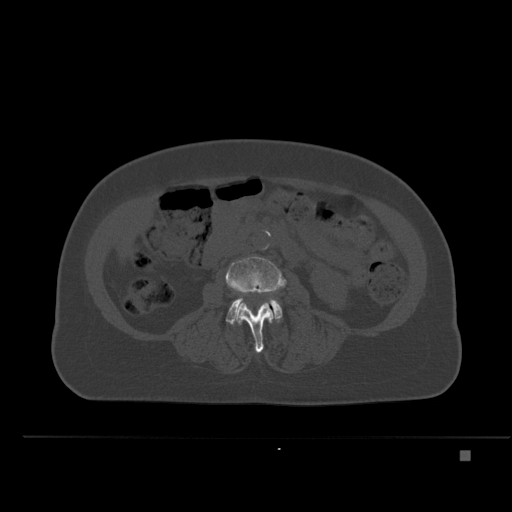
CT including the spine, one axial slice. Slice 191 of 477 in the series (ordered by position). Bone window (W 1800 / L 400 HU). 1.5 mm slice thickness. 512 × 512 image matrix, field of view 422 × 422 mm. Female patient, age 74 years. From the clinical record (not read from this slice): primary cancer: colon.
Annotated regions visible in this slice (semi-automatic segmentation, software-assisted and operator-edited):
- L3 vertebra: bounding box (x1, y1, x2, y2) in pixels: (225, 257, 287, 353)
- L4 vertebra: (226, 298, 282, 324)